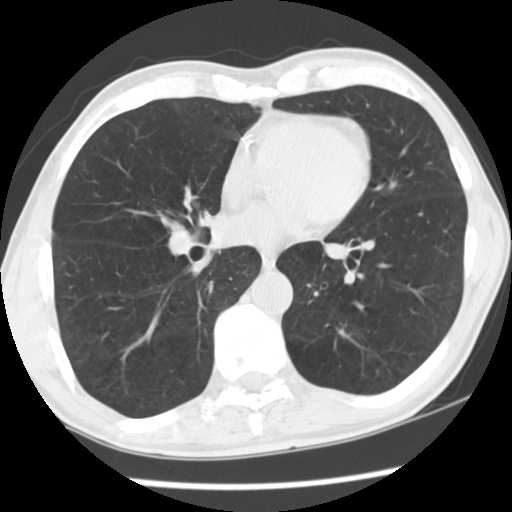
Axial slice from a low-dose chest CT screening exam, second annual screen, lung window (W 1500 / L -600 HU), 2.5 mm slice thickness, standard (soft-tissue) reconstruction kernel (STANDARD), slice 77 of 133 in the series. Male participant, aged 63 years at enrolment.
Lesion marked by an expert reader, bounding box (x1, y1, x2, y2) in pixels: (405, 202, 438, 231). Screening reader's record for this exam: no non-calcified nodule ≥4 mm recorded. Later outcome: lung cancer diagnosed 577 days after this screen — squamous cell carcinoma, NOS, left lower lobe, poorly differentiated (G3), stage IA (AJCC 6th edition), 4 mm at pathology.